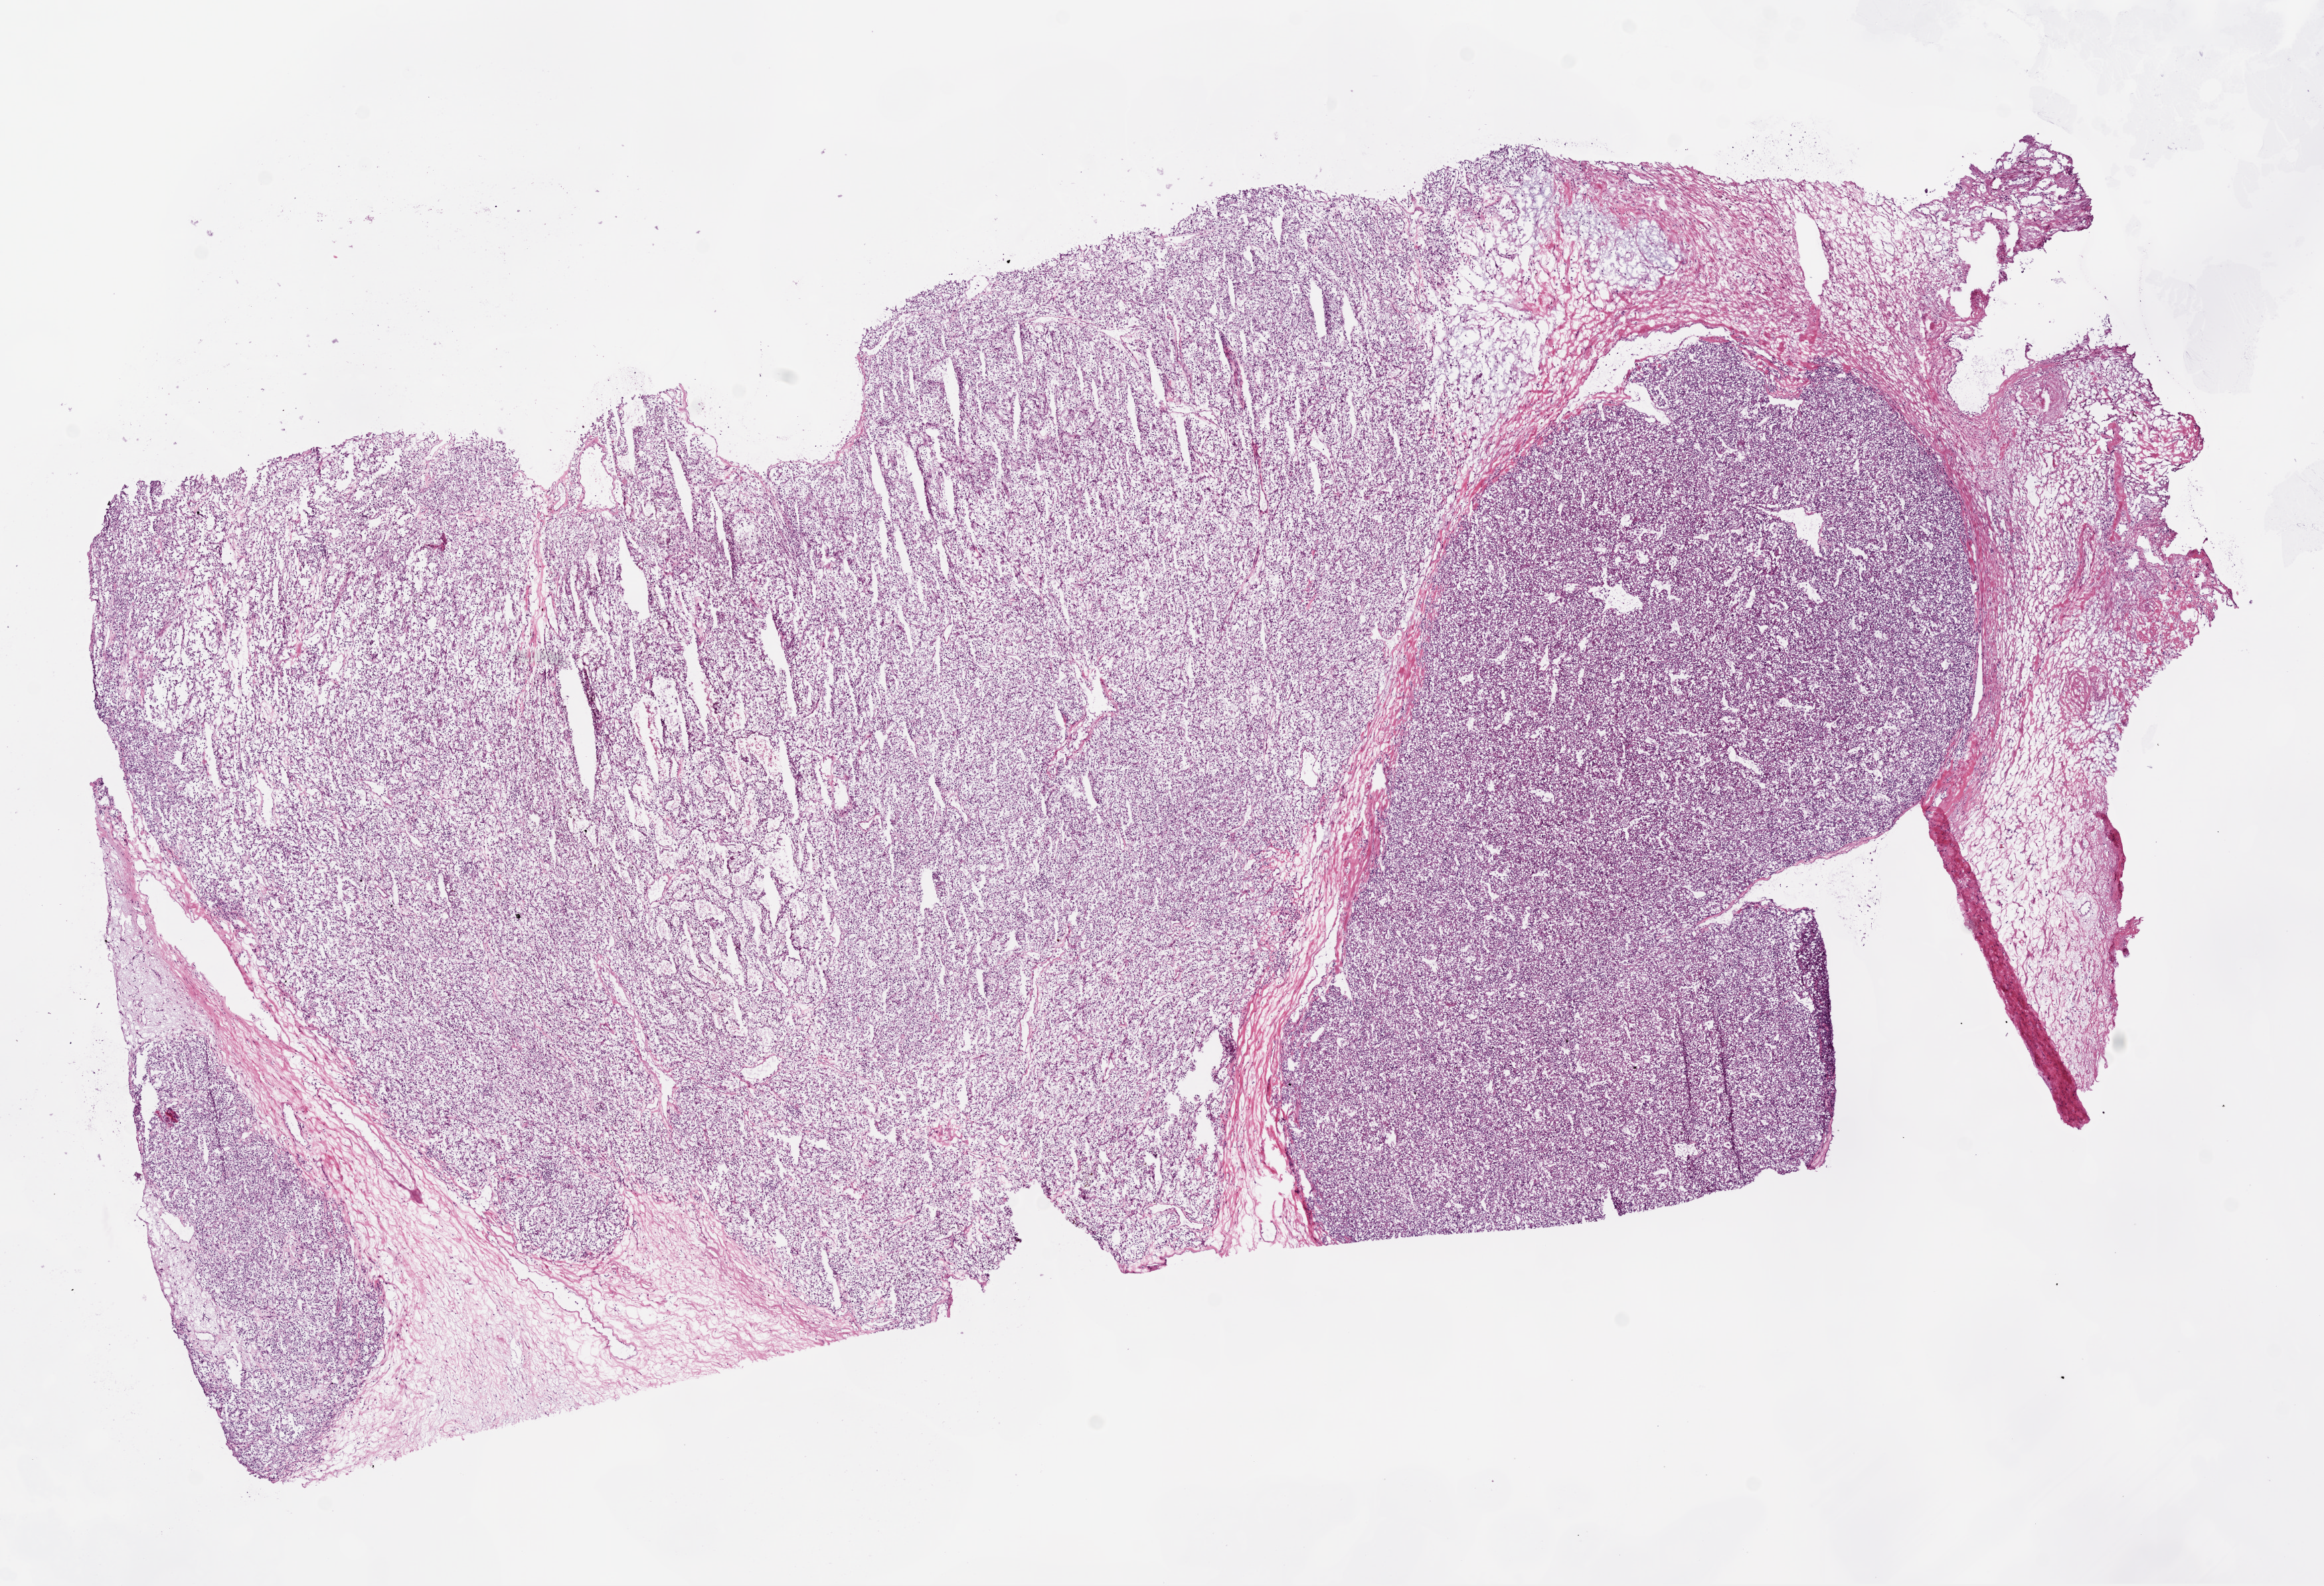
Hematoxylin and eosin (H&E) stained whole-slide image — whole scanned area (about 14.0 x 9.6 mm) shown as a low-resolution overview. Frozen section. Primary tumour sample from the kidney. Patient: male, age at initial diagnosis 57 years. Histologic grade: G2 (moderately differentiated). Composition of this section per pathologist review: tumour cells 80%, tumour nuclei 85%, normal cells 0%, stromal cells 20%, necrosis 0%.
Diagnosis: Clear cell adenocarcinoma, NOS. Laterality: right. AJCC pathologic stage: I (6th edition).